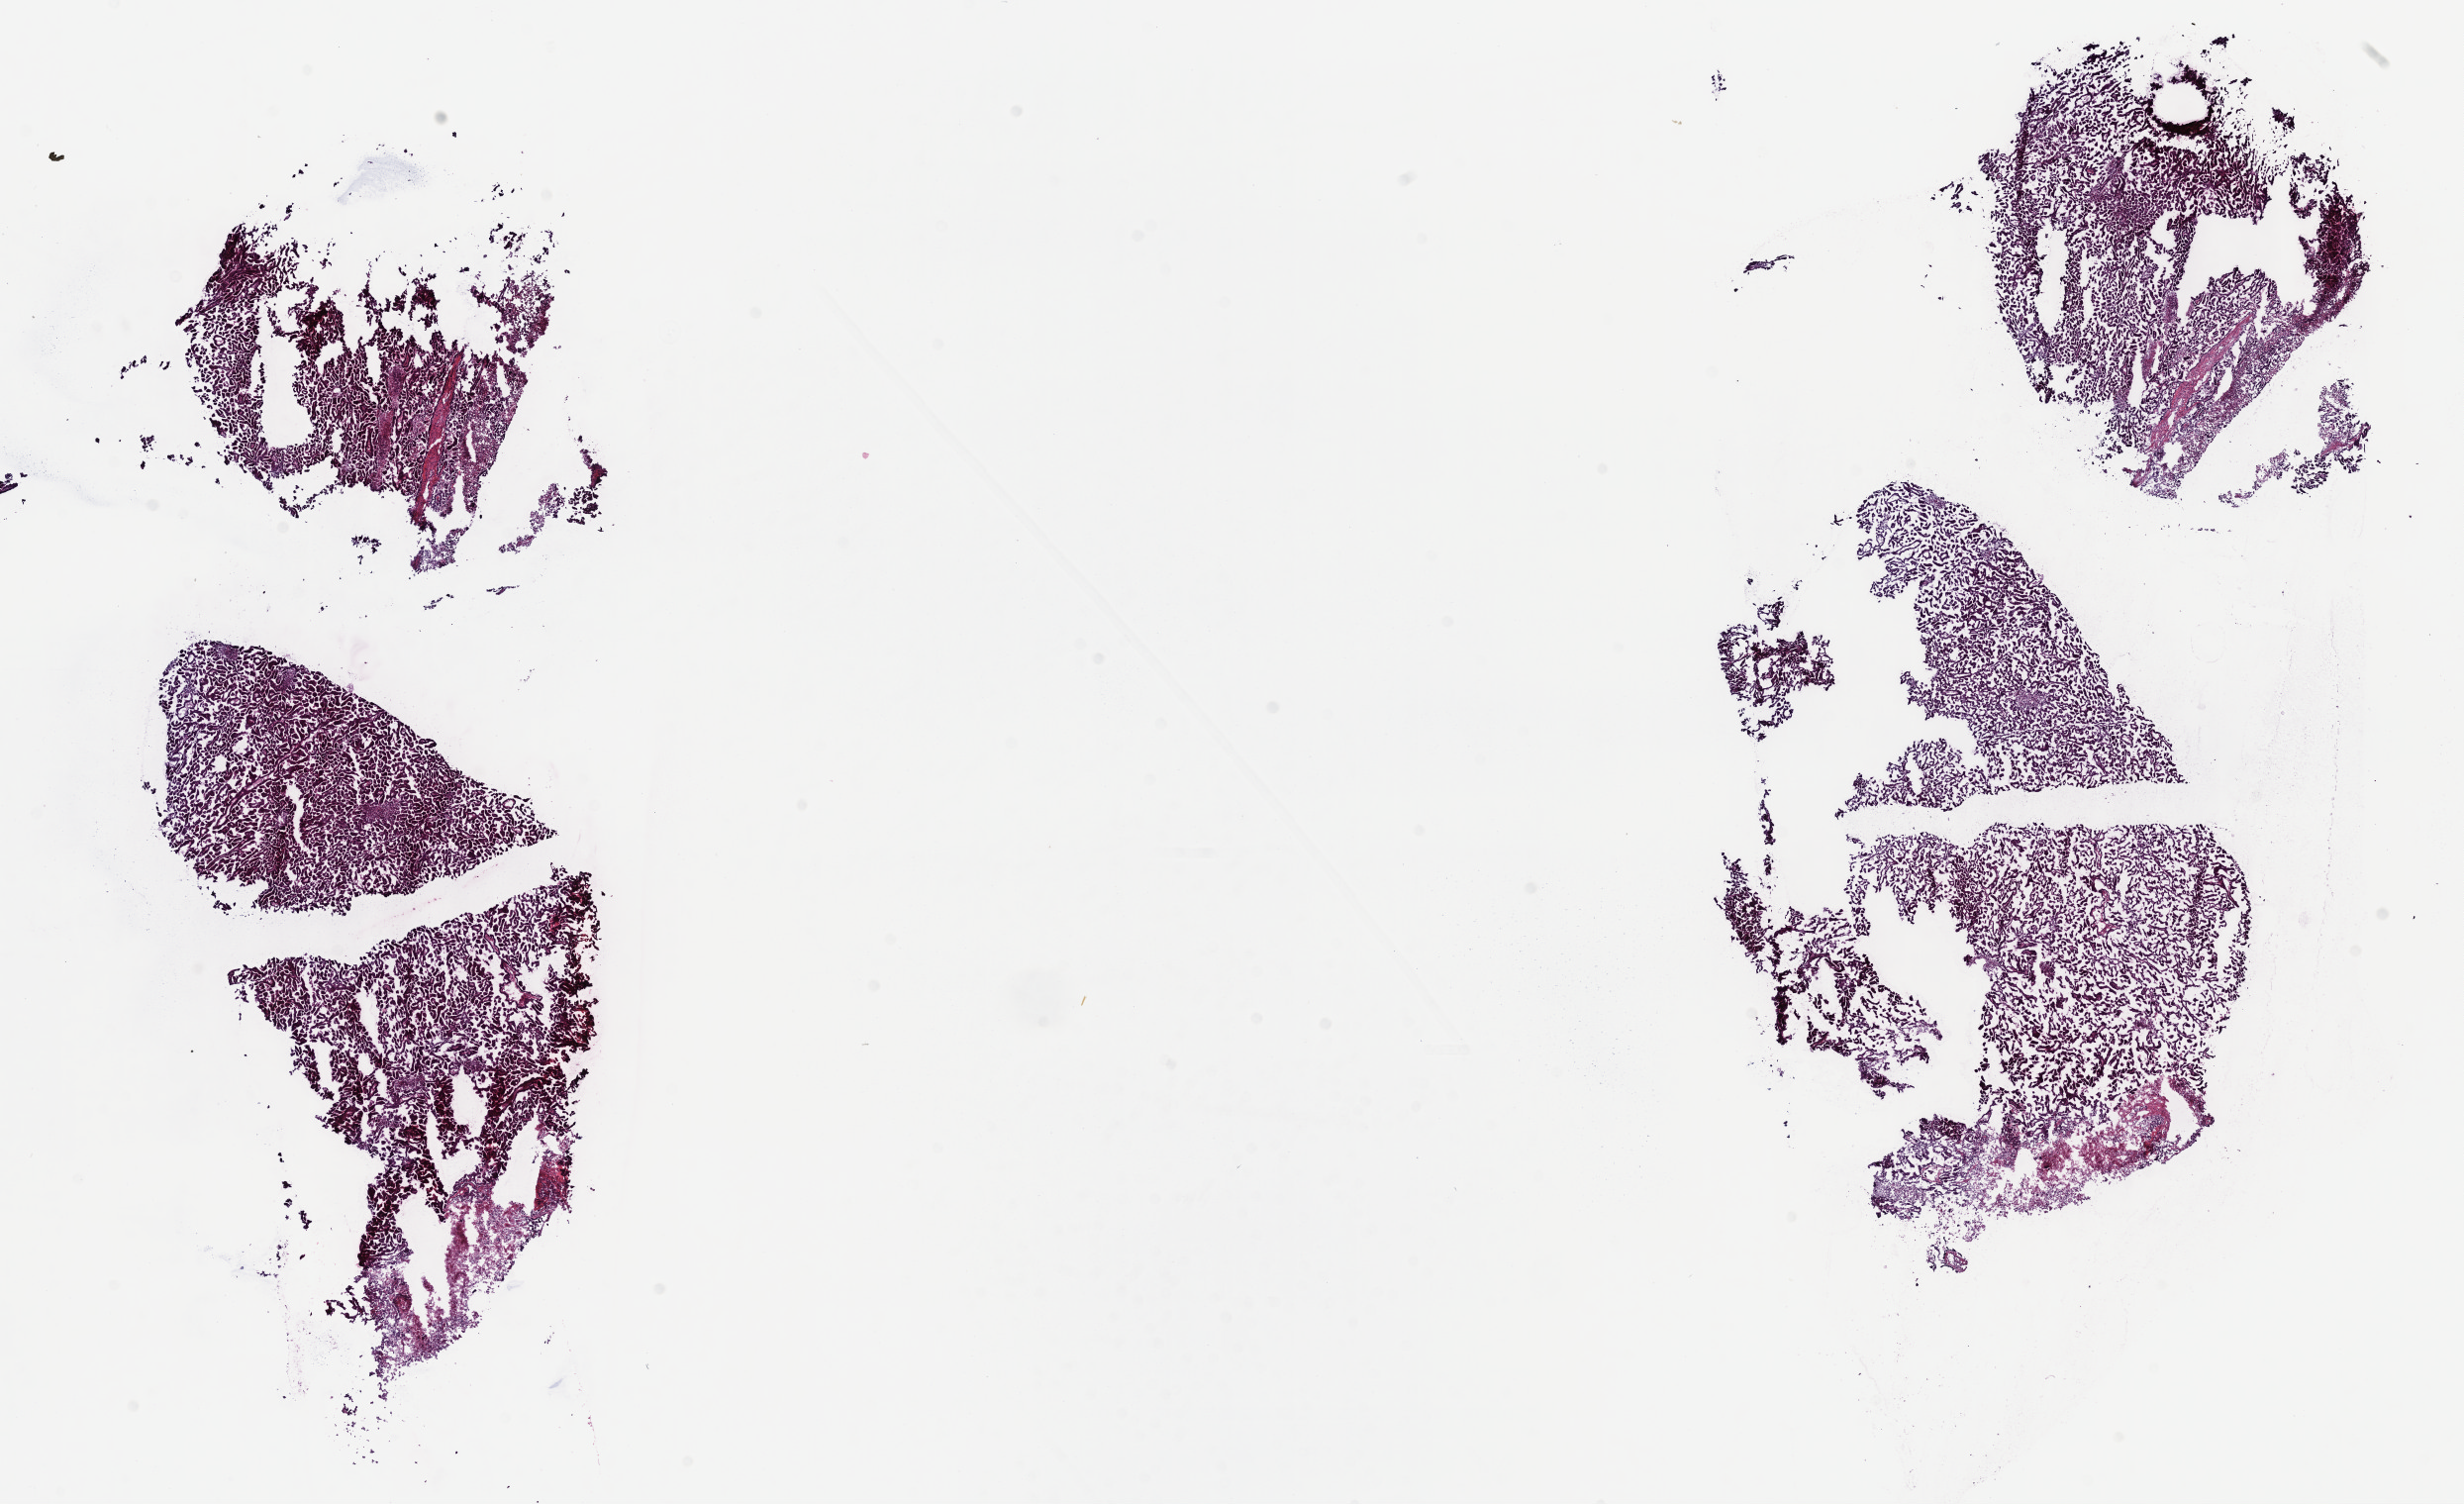
Hematoxylin and eosin (H&E) stained whole-slide image — shown as a low-resolution overview of the whole scanned area (about 20.1 x 12.3 mm, acquisition: 40x scan), frozen section from the top of the tissue portion, kidney, primary tumour sample. Male, age 67 years at initial diagnosis. Slide review estimates, as recorded: tumour cells 89%, tumour nuclei 94%, normal cells 0%, stromal cells 4%, necrosis 7%. Inflammatory infiltration, as recorded: lymphocyte infiltration 3%, monocyte infiltration 2%, neutrophil infiltration 0%.
Histologic diagnosis: Papillary adenocarcinoma, NOS. AJCC pathologic stage: II (6th edition).